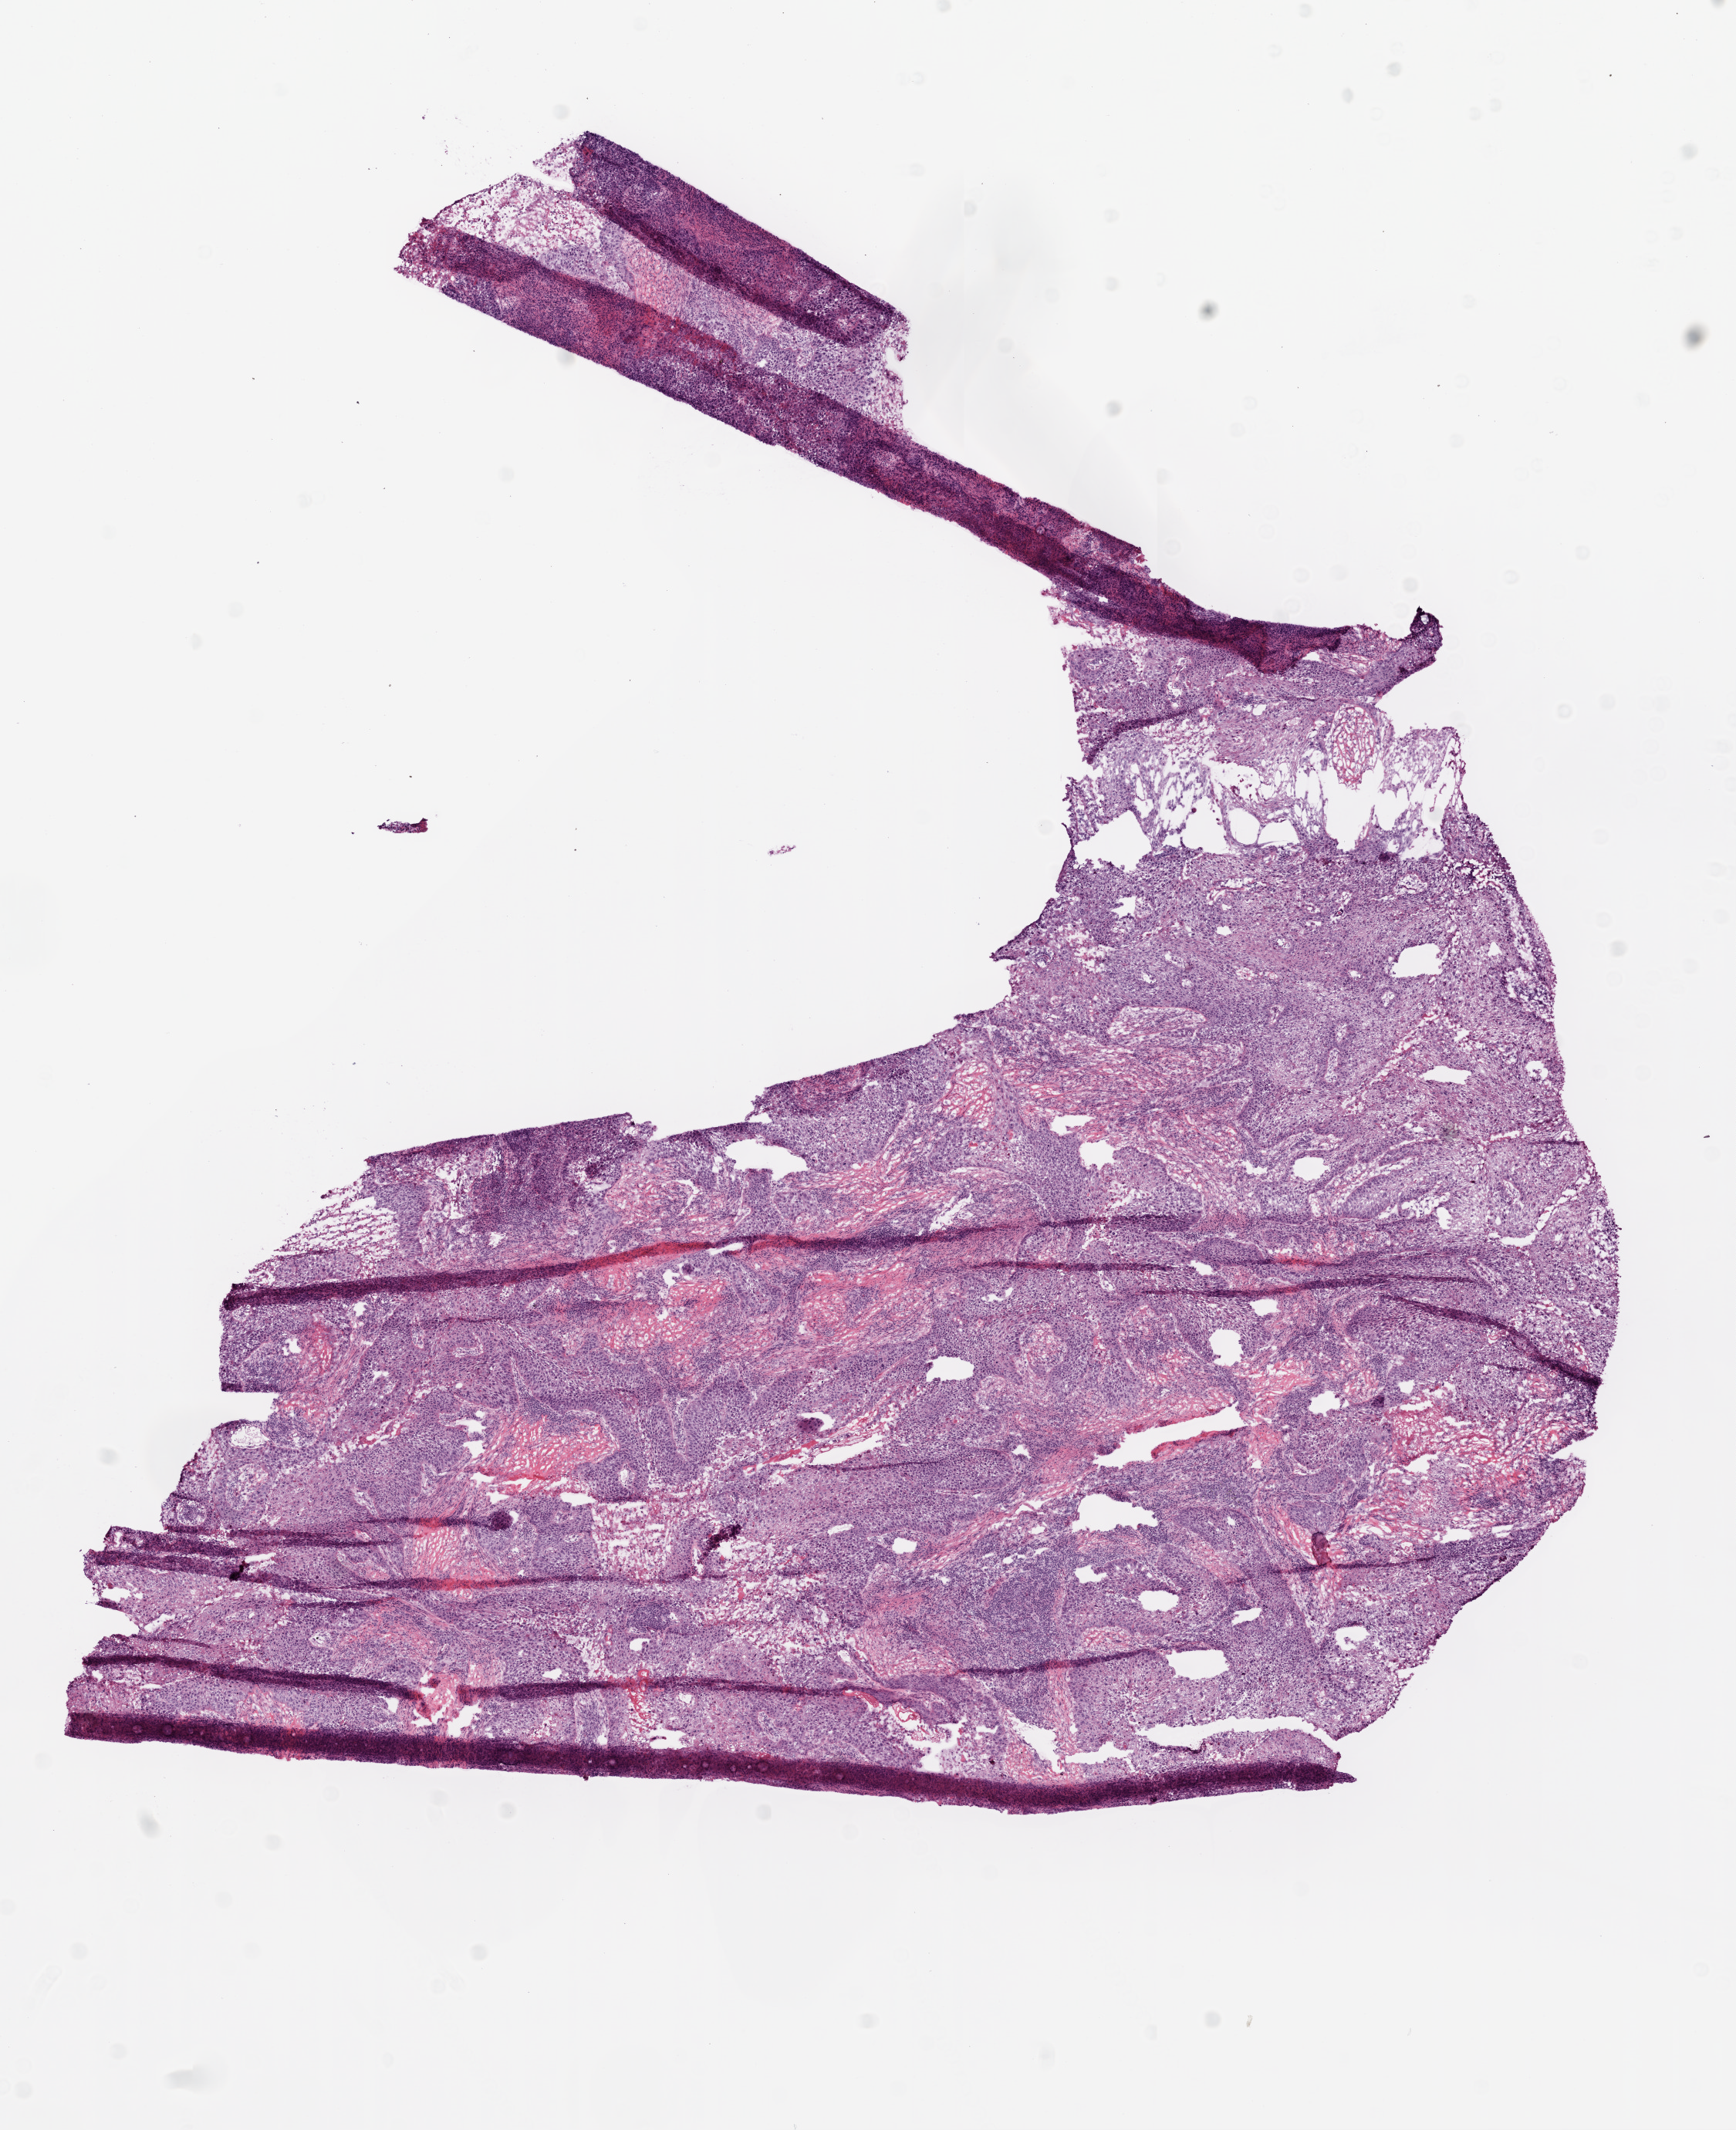
Whole-slide histology image, H&E, shown as a low-resolution overview of the whole scanned area (about 9.0 x 11.1 mm, from a 20x scan). Frozen section from the top of the tissue portion. Lung, primary tumour sample. Male patient; age at initial diagnosis 66 years. Composition of this section per pathologist review: tumour cells 70%, tumour nuclei 85%, normal cells 0%, stromal cells 10%, necrosis 20%.
AJCC pathologic stage: IIIA. Histologic diagnosis: Squamous cell carcinoma, NOS (lower lobe, lung).